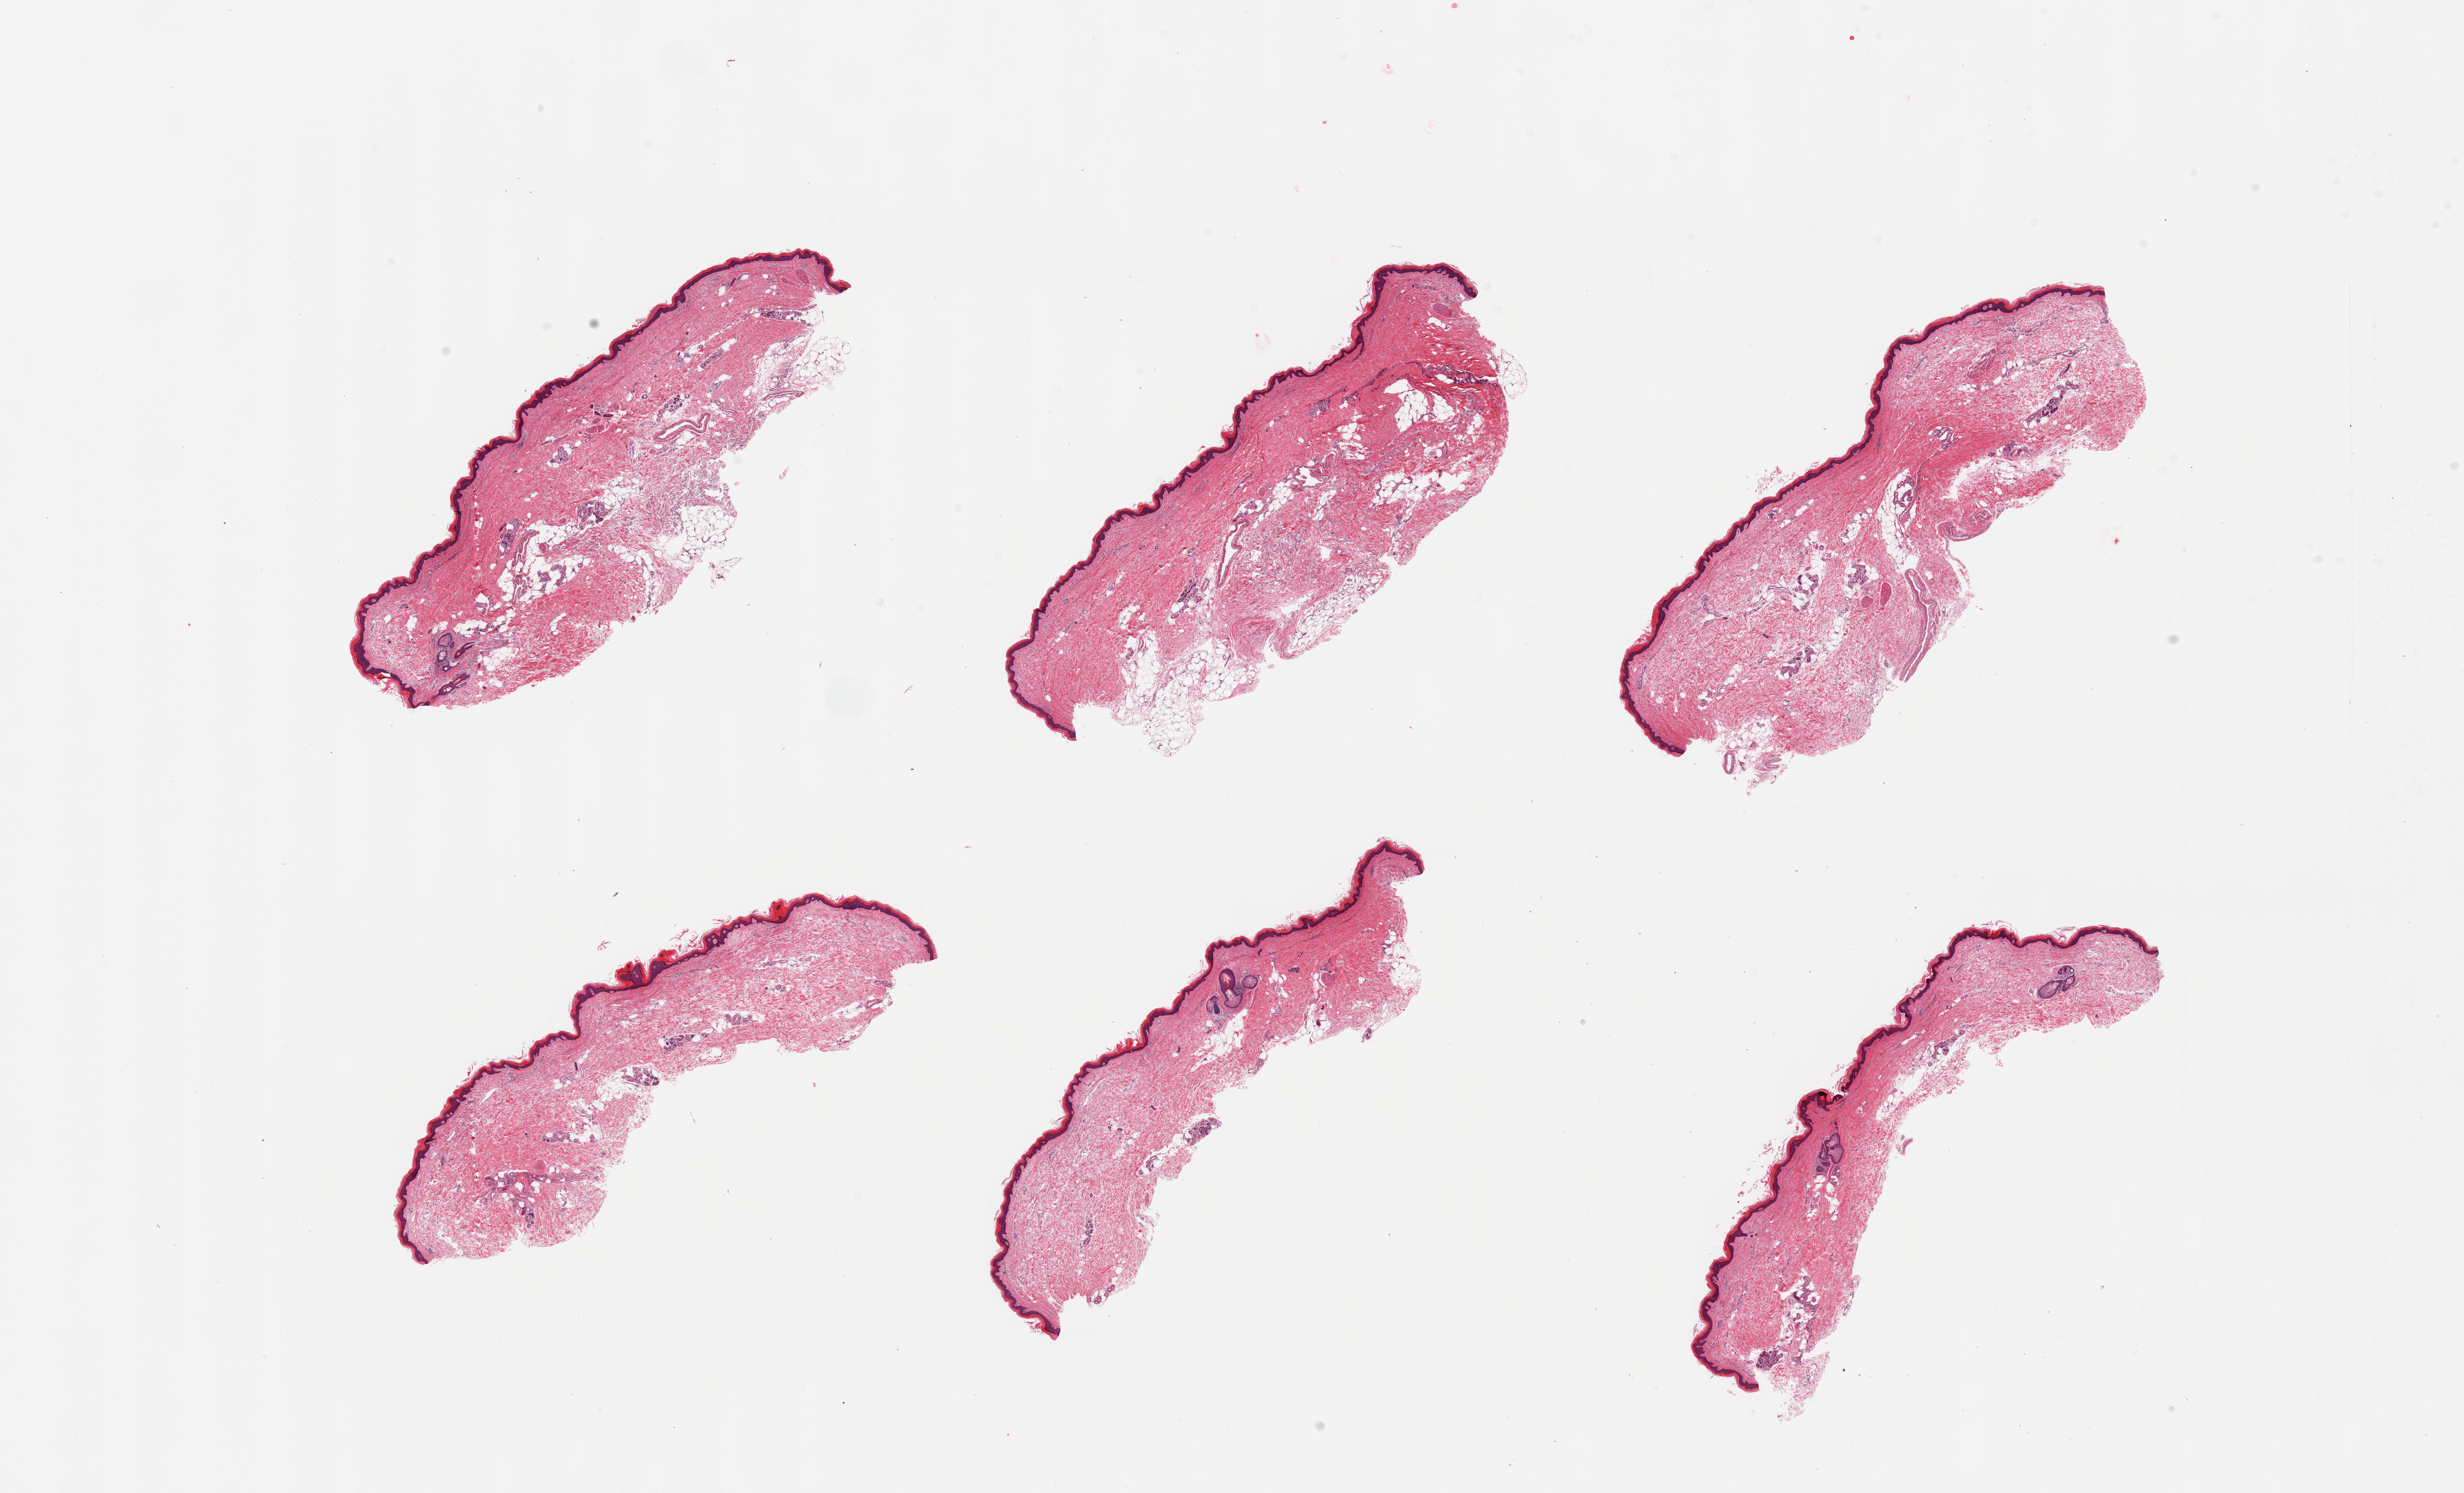
Digitized H&E-stained section — whole scanned area (about 31.5 x 19.1 mm, from a 20x scan) shown as a low-resolution overview; PAXgene-fixed, paraffin-embedded tissue; section of skin of lower leg (target tissue); tissue donor sample. Male donor.
Pathologist's review note for this sample: 6 pieces; predominantly well trimmed, but with 5-20% internal (mostly) and attached fat, epidermis measures 32 microns.